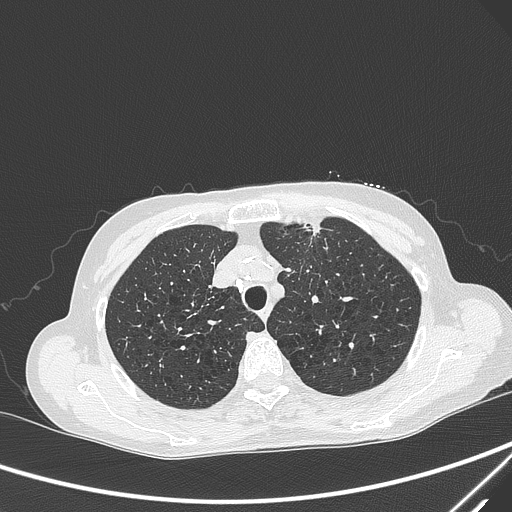
Chest CT, one axial slice. Slice 237 of 299 in the series (ordered by position). Lung window (W 1500 / L -600 HU). 1 mm slice thickness. 512 × 512 image matrix, field of view 350 × 350 mm. Female patient, age 71 years. Case-level facts recorded for this patient, not image findings: clinical TNM (as recorded): T1c N0 M0.
Outlined on this slice (rectangle marked by the reading radiologist):
- lung tumour (recorded histology: adenocarcinoma): bounding box <296,216,330,247> (left, top, right, bottom; pixels)